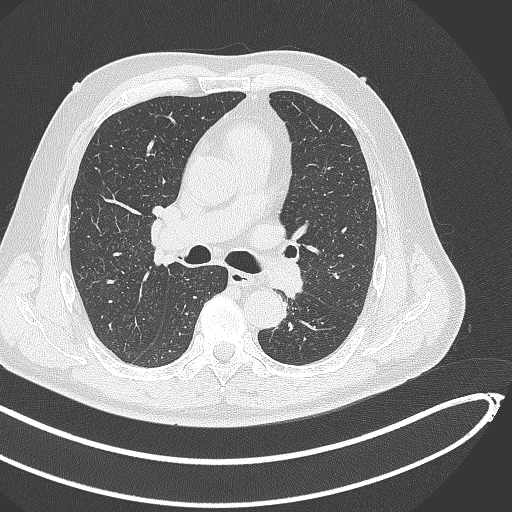
Chest CT, one axial slice; reconstruction kernel B70f; lung window (W 1500 / L -600 HU); 1 mm slice thickness; 512 × 512 image matrix, field of view 400 × 400 mm. Male patient, age 64 years. From the clinical record (not read from this slice): clinical TNM (as recorded): T1c N0 M0; histopathological grade: G2.
Annotated regions visible in this slice (bounding box drawn by a radiologist):
- lung tumour (recorded histology: squamous cell carcinoma): bounding box (x1, y1, x2, y2) in pixels: (262, 250, 305, 300)